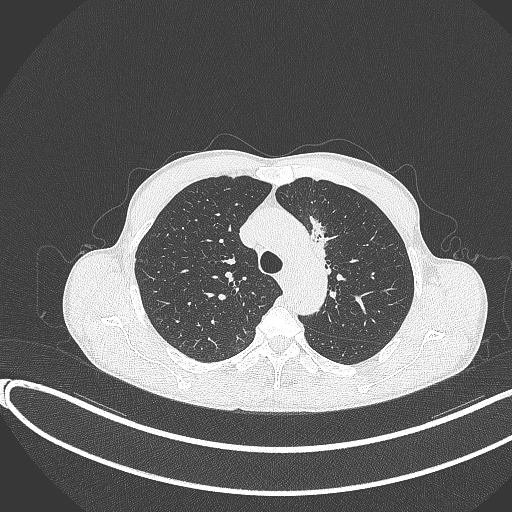
Chest CT, one axial slice. Lung window (W 1500 / L -600 HU). 512 × 512 image matrix, field of view 400 × 400 mm. Patient: male, 58 years. Case-level facts recorded for this patient, not image findings: clinical TNM (as recorded): T1c N1 M0.
Outlined on this slice (rectangle marked by the reading radiologist):
- lung tumour (recorded histology: adenocarcinoma): bounding box [x1, y1, x2, y2] px = [303, 211, 341, 269]